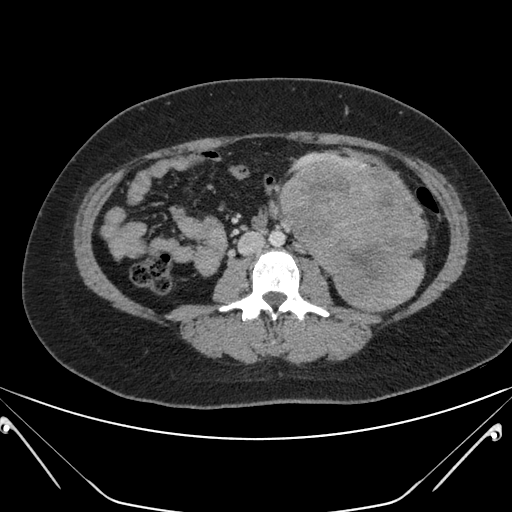
Contrast-enhanced abdominal CT, one axial slice; position 91 of 168 along the scan axis; 120 kVp; intravenous contrast given; soft-tissue window (W 400 / L 40 HU); 512 × 512 image matrix, field of view 394 × 394 mm. Patient: female, 26 years. Case-level facts recorded for this patient, not image findings: diagnosis: adrenocortical carcinoma; tumour side: left adrenal; tumour size at pathology: 28 cm; Ki-67 index: 20 %; stage (as recorded): 2.
Structures marked on this image (semi-automatically segmented with operator editing):
- mass: bounding box [x1, y1, x2, y2] px = [281, 160, 424, 310]